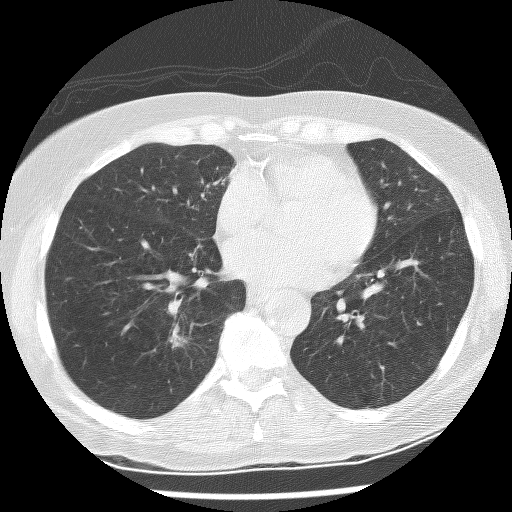
Low-dose screening chest CT, one axial slice; slice 103 of 247 in the series (ordered by position); lung window (W 1500 / L -600 HU); 2.5 mm slice thickness; 512 × 512 image matrix, field of view 300 × 300 mm.
Outlined on this slice (expert manual segmentation):
- lesion 1 (tumor, lower lobe of right lung): bounding box [x1, y1, x2, y2] px = [170, 324, 191, 348]